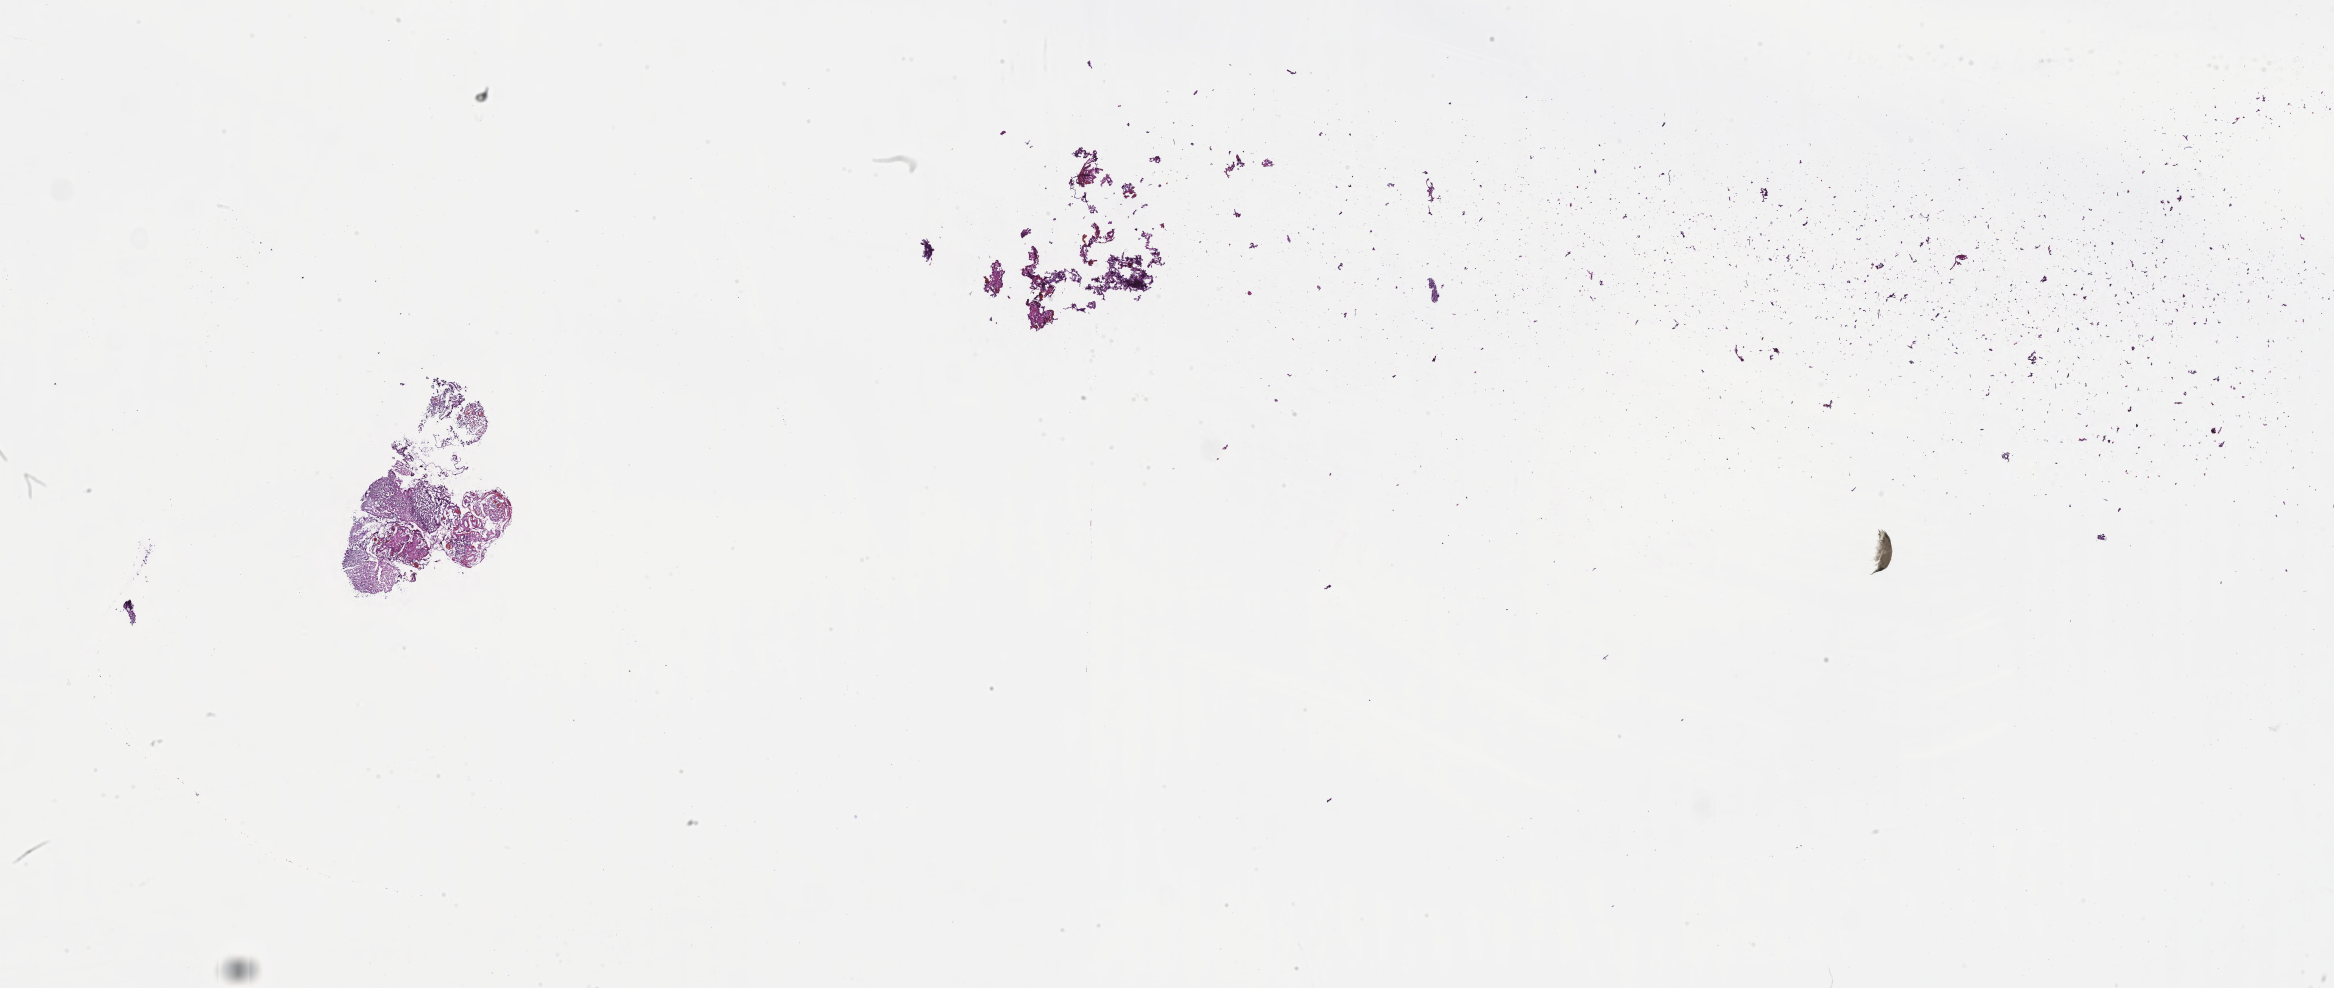
Digitized H&E-stained section of tumor tissue from the brain, low-resolution overview of the scanned area, about 37.7 x 16.0 mm; cryosection (OCT / tissue freezing medium). Male patient, age 450 days (about 1.2 years).
• diagnosis: Atypical teratoid/rhabdoid tumor